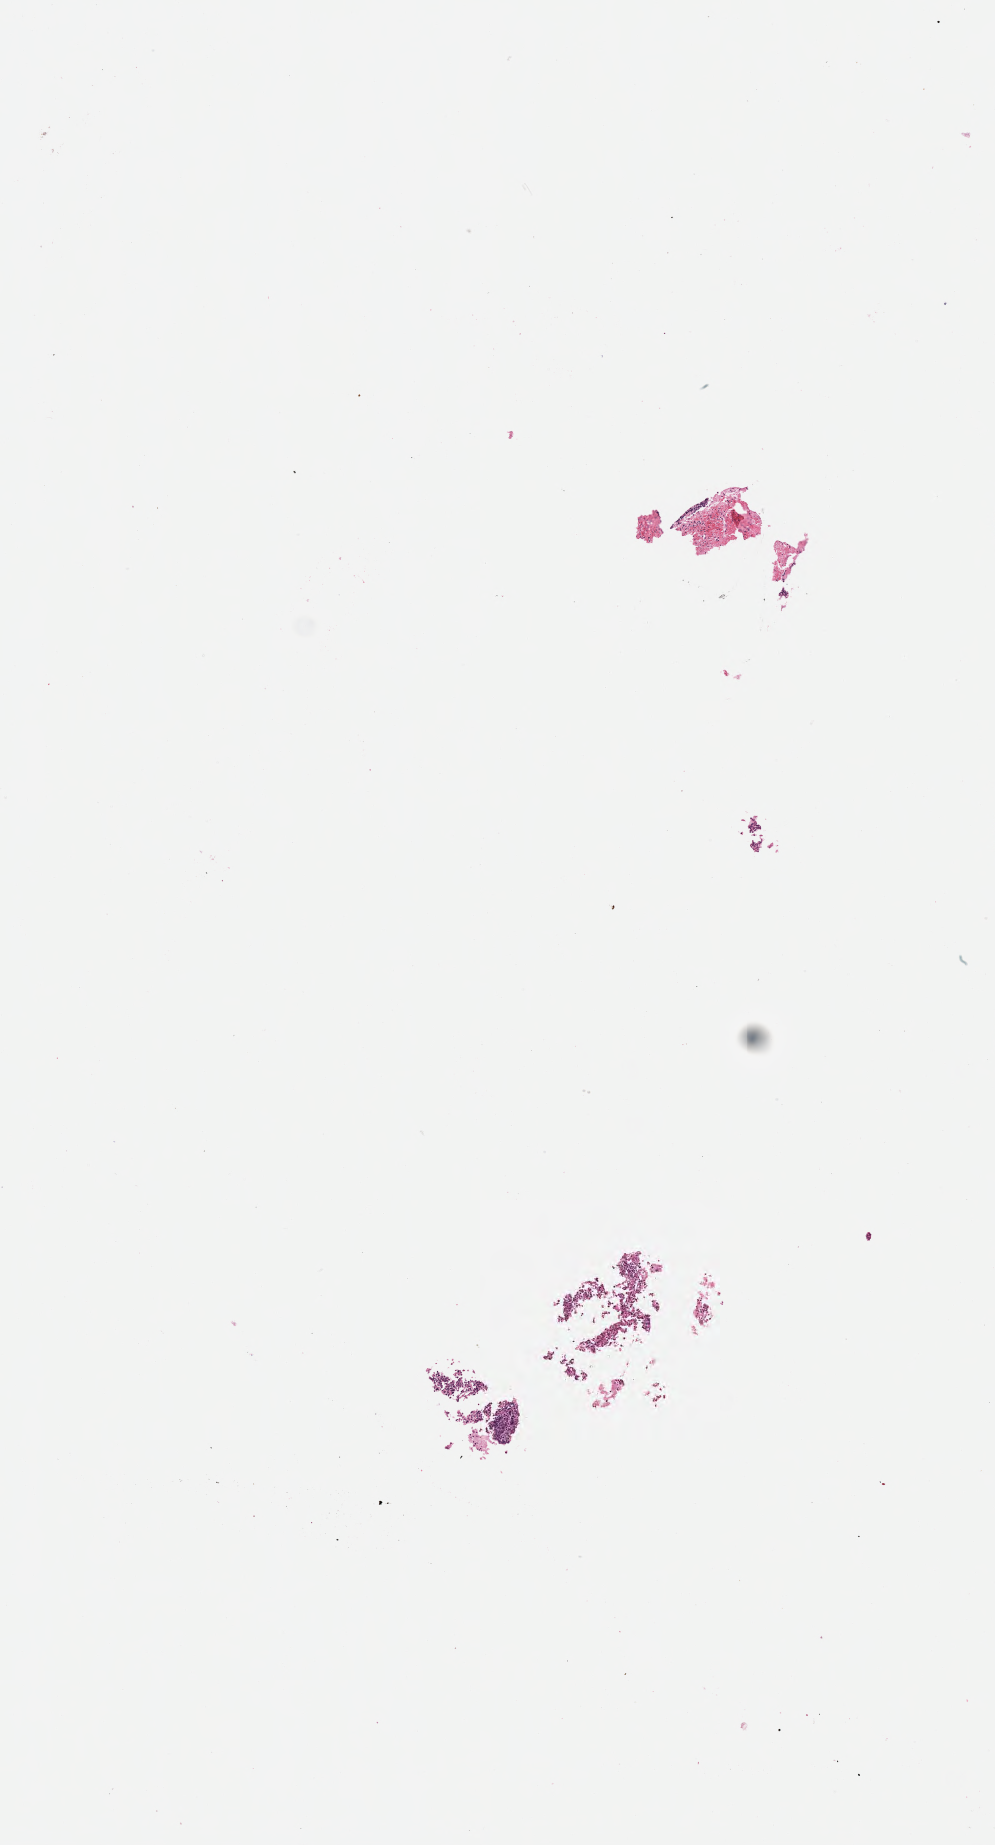
Hematoxylin and eosin (H&E) whole-slide image, a low-resolution overview of the entire scanned area, about 4.0 x 7.5 mm. Formalin-fixed, paraffin-embedded (FFPE) tissue. Specimen: primary tumor. Anatomic site: liver. Patient: male, age at initial diagnosis 5 years. Slide review estimates, as recorded: tumor cells 40%, tumor nuclei 60%, stromal cells 50%, necrosis 10%, normal cells 0%. Inflammatory infiltration, as recorded: lymphocyte infiltration 30%, monocyte infiltration 30%, neutrophil infiltration 10%.
• histologic diagnosis: Burkitt lymphoma, NOS
• Ann Arbor stage (patient): Stage III